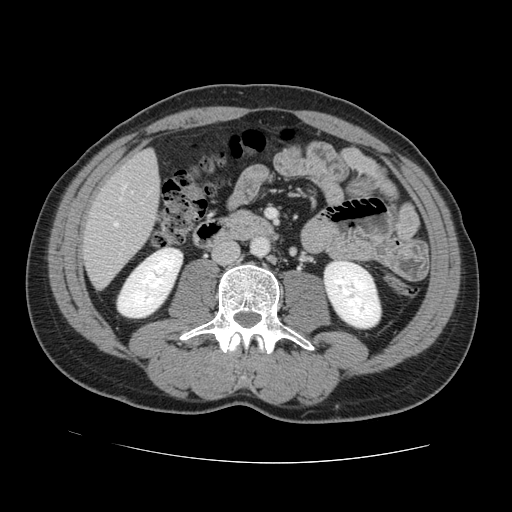
Contrast-enhanced abdominal CT, one axial slice. Slice 34 of 131 in the series (ordered by position). 120 kVp. Intravenous contrast given. Soft-tissue window (W 400 / L 40 HU). 2.5 mm slice thickness. 512 × 512 image matrix. Male patient, age 40 years. Case-level facts recorded for this patient, not image findings: diagnosis: colorectal cancer liver metastases, imaged before liver resection; multiple liver metastases: yes; largest metastasis: 2.9 cm.
Structures marked on this image (manually delineated by an expert):
- hepatic veins: box from (x=114, y=185) to (x=126, y=226) px
- liver: (x=83, y=151)–(x=160, y=287)
- planned liver remnant (the part of the liver to remain after resection): (x=143, y=152)–(x=154, y=160)